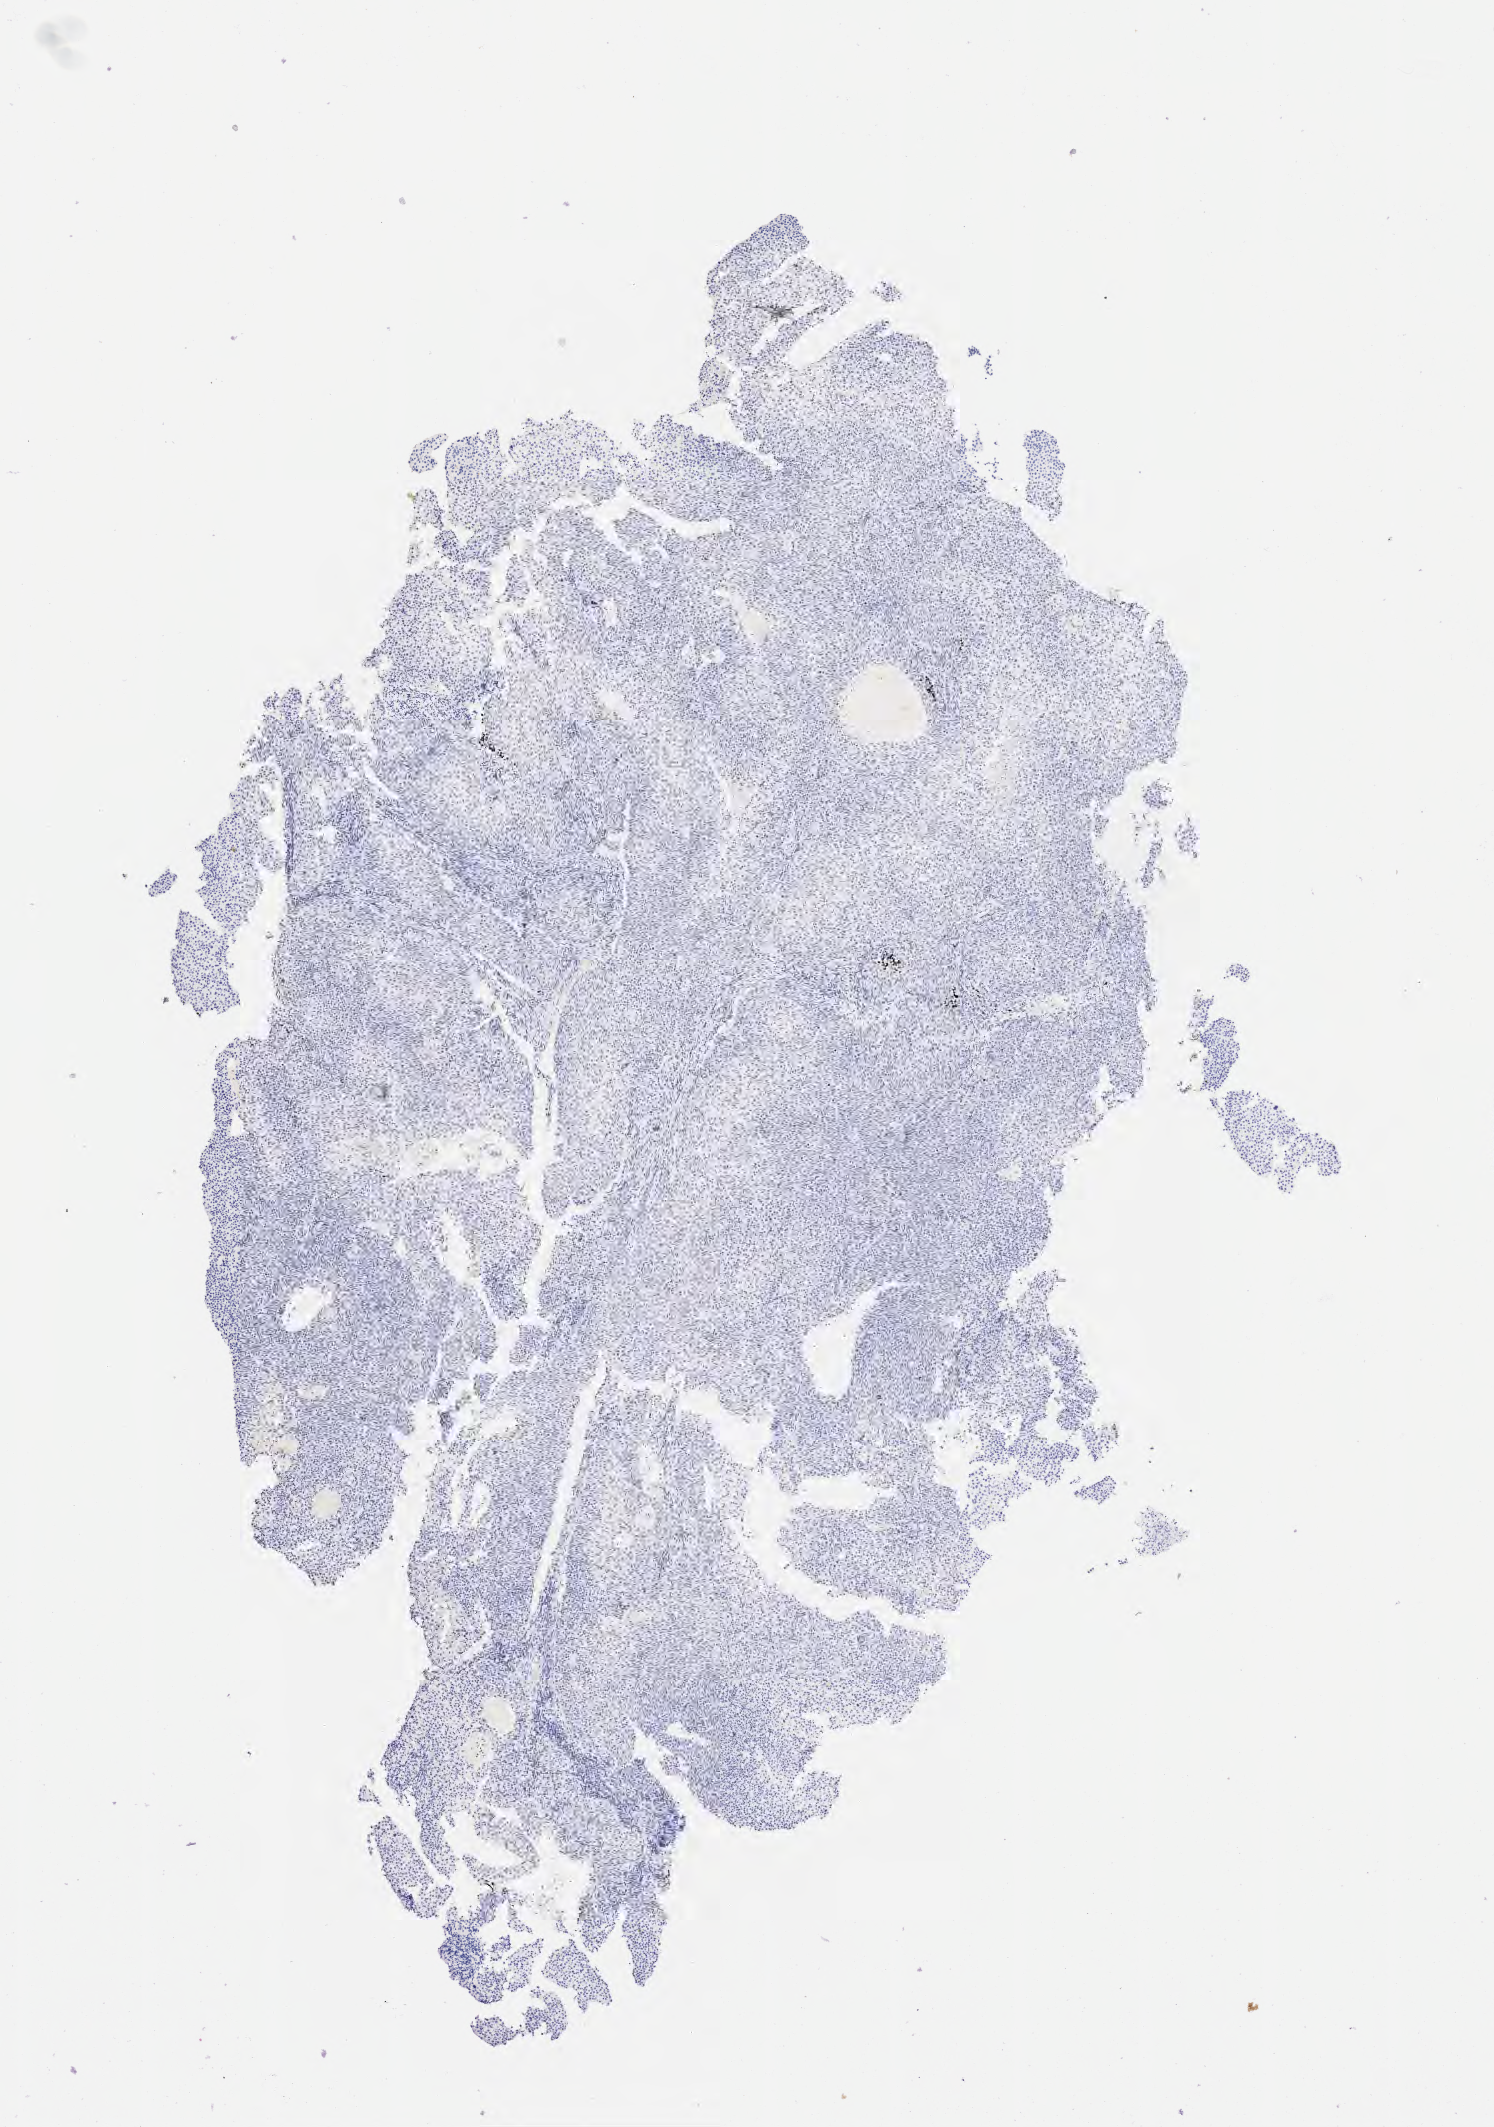
Whole-slide image, immunohistochemical stain for p40, a low-resolution overview of the entire scanned area, about 6.0 x 8.6 mm. Tumor tissue. Site: cervix. Patient: female, aged 39.
Diagnosis: Squamous cell carcinoma, large cell, nonkeratinizing, NOS.